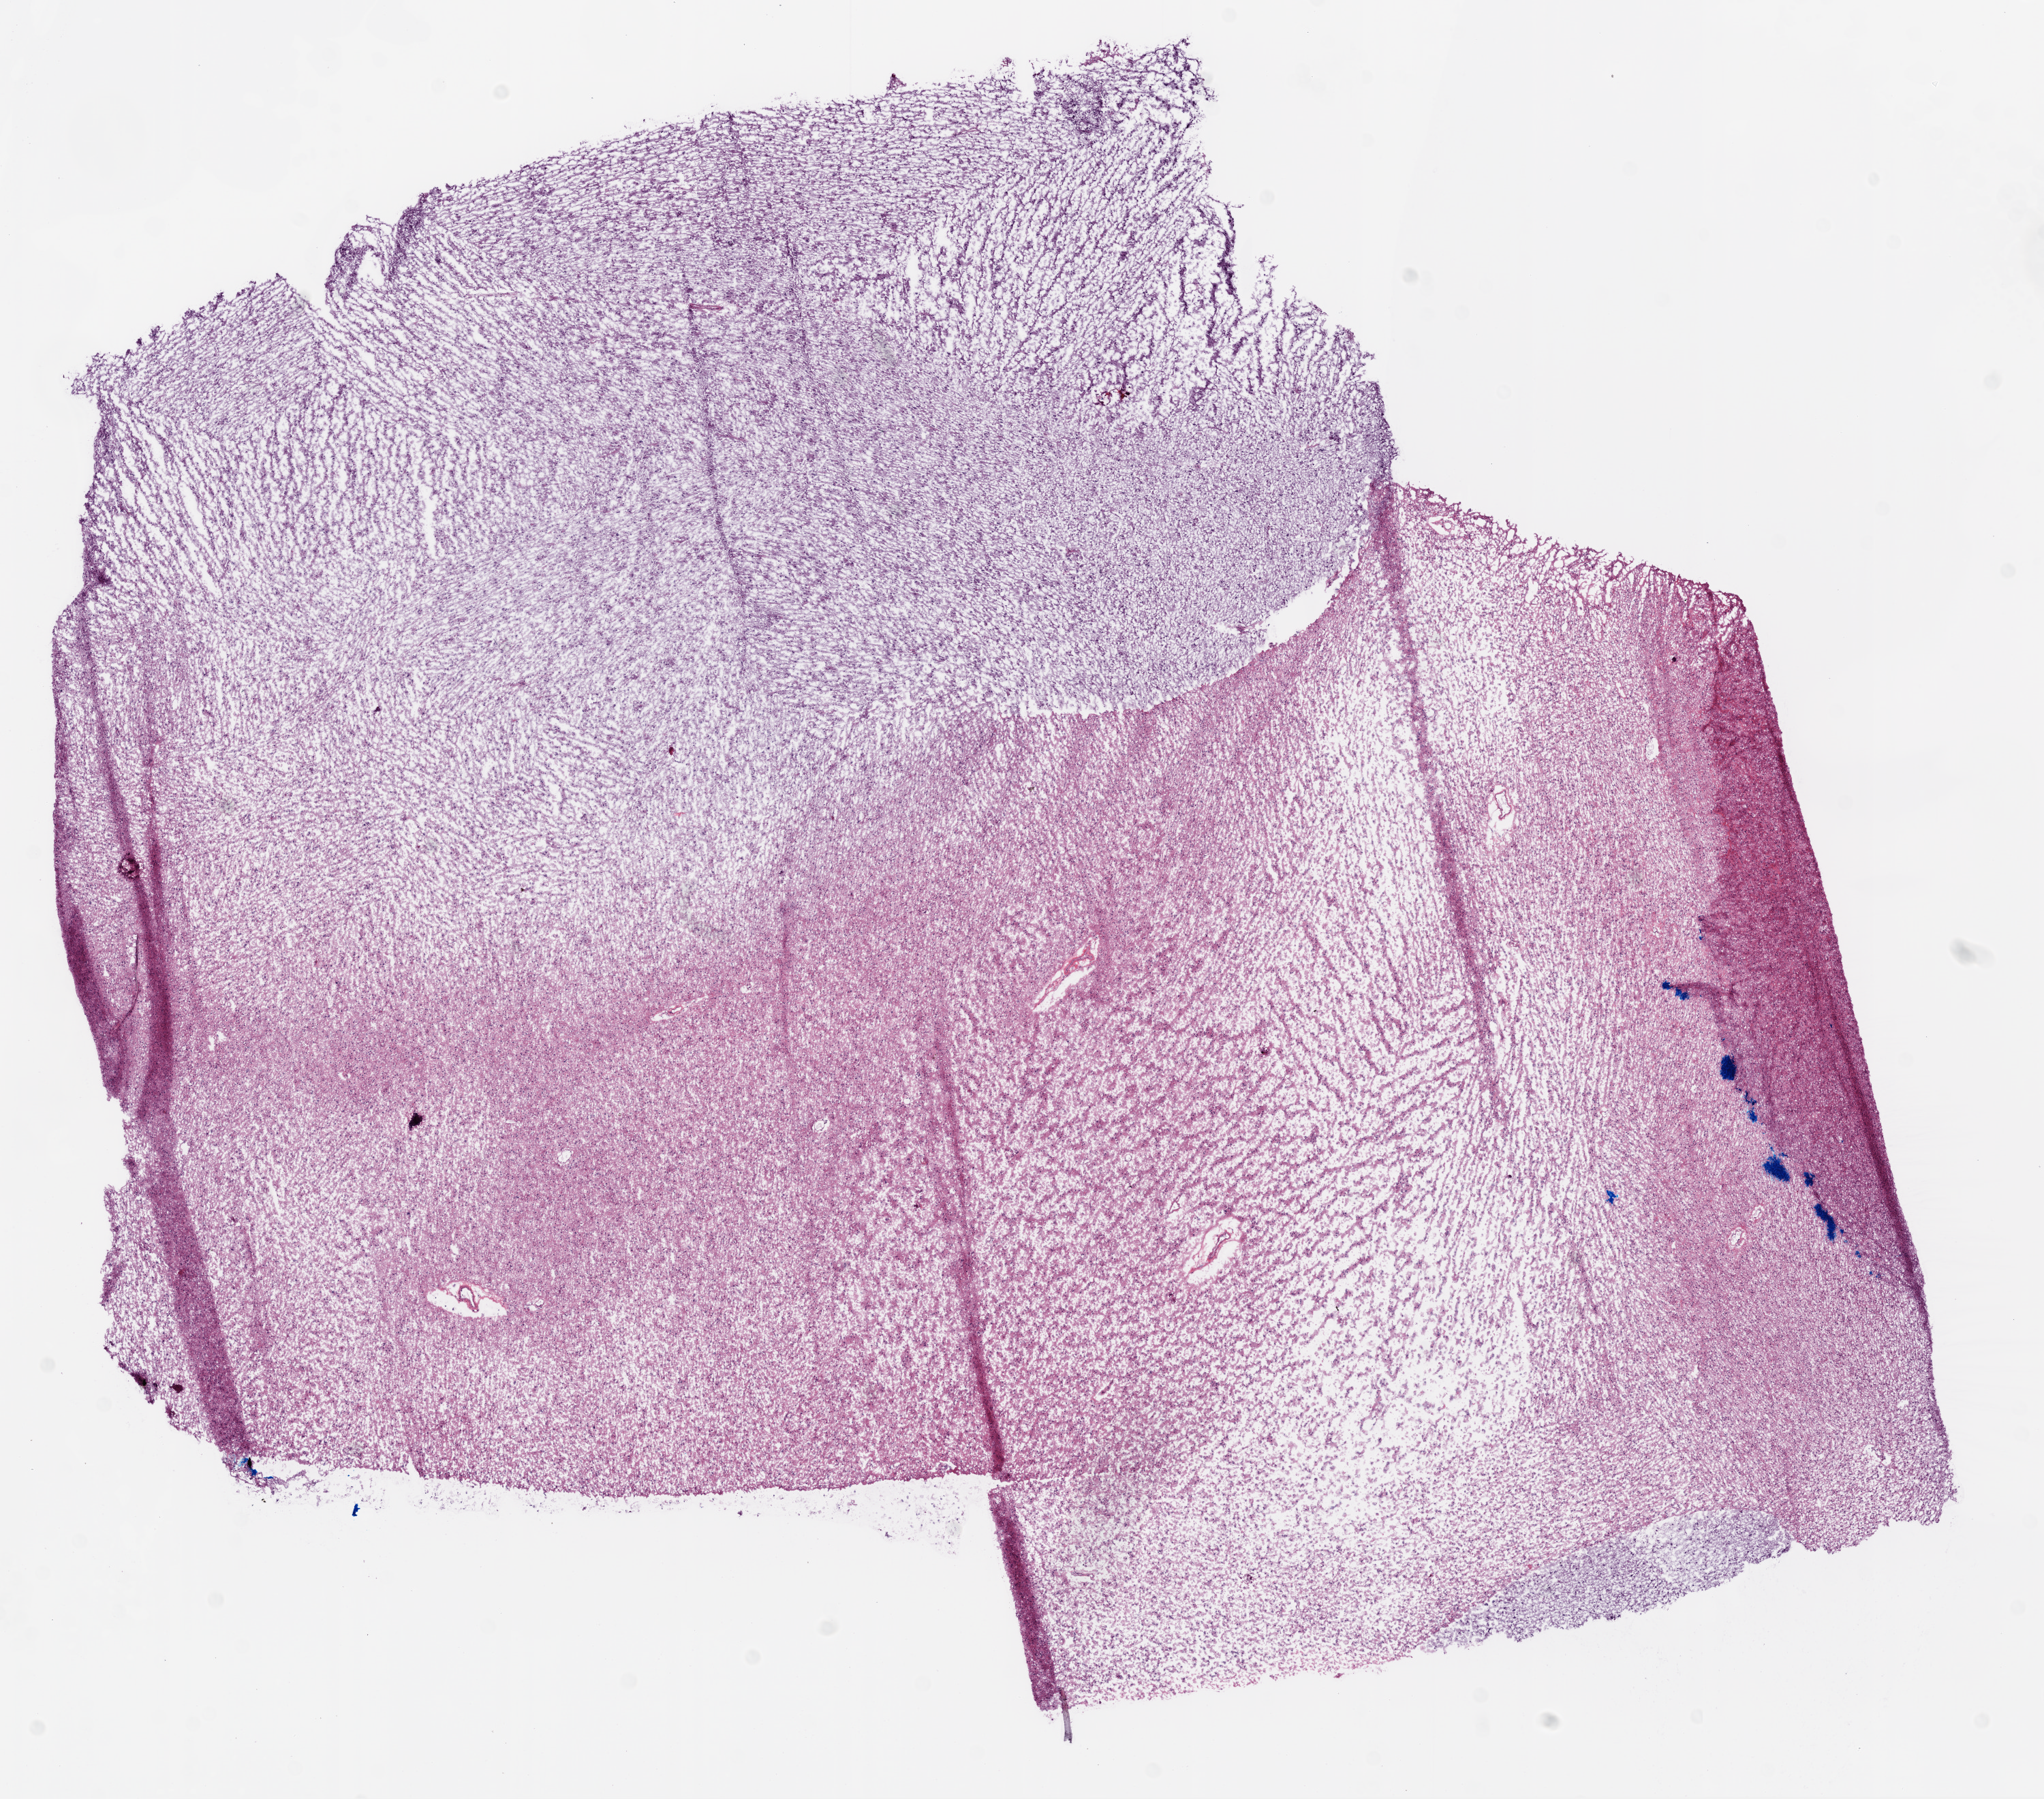
Whole-slide histology image, H&E — whole scanned area (about 12.0 x 10.6 mm, slide scanned at 20x) shown as a low-resolution overview, frozen section, primary tumour sample from the brain. Patient: male, age at initial diagnosis 39 years. Slide review estimates, as recorded: tumour cells 80%, tumour nuclei 80%, normal cells 20%, stromal cells 0%, necrosis 0%.
Diagnosis: Glioblastoma.